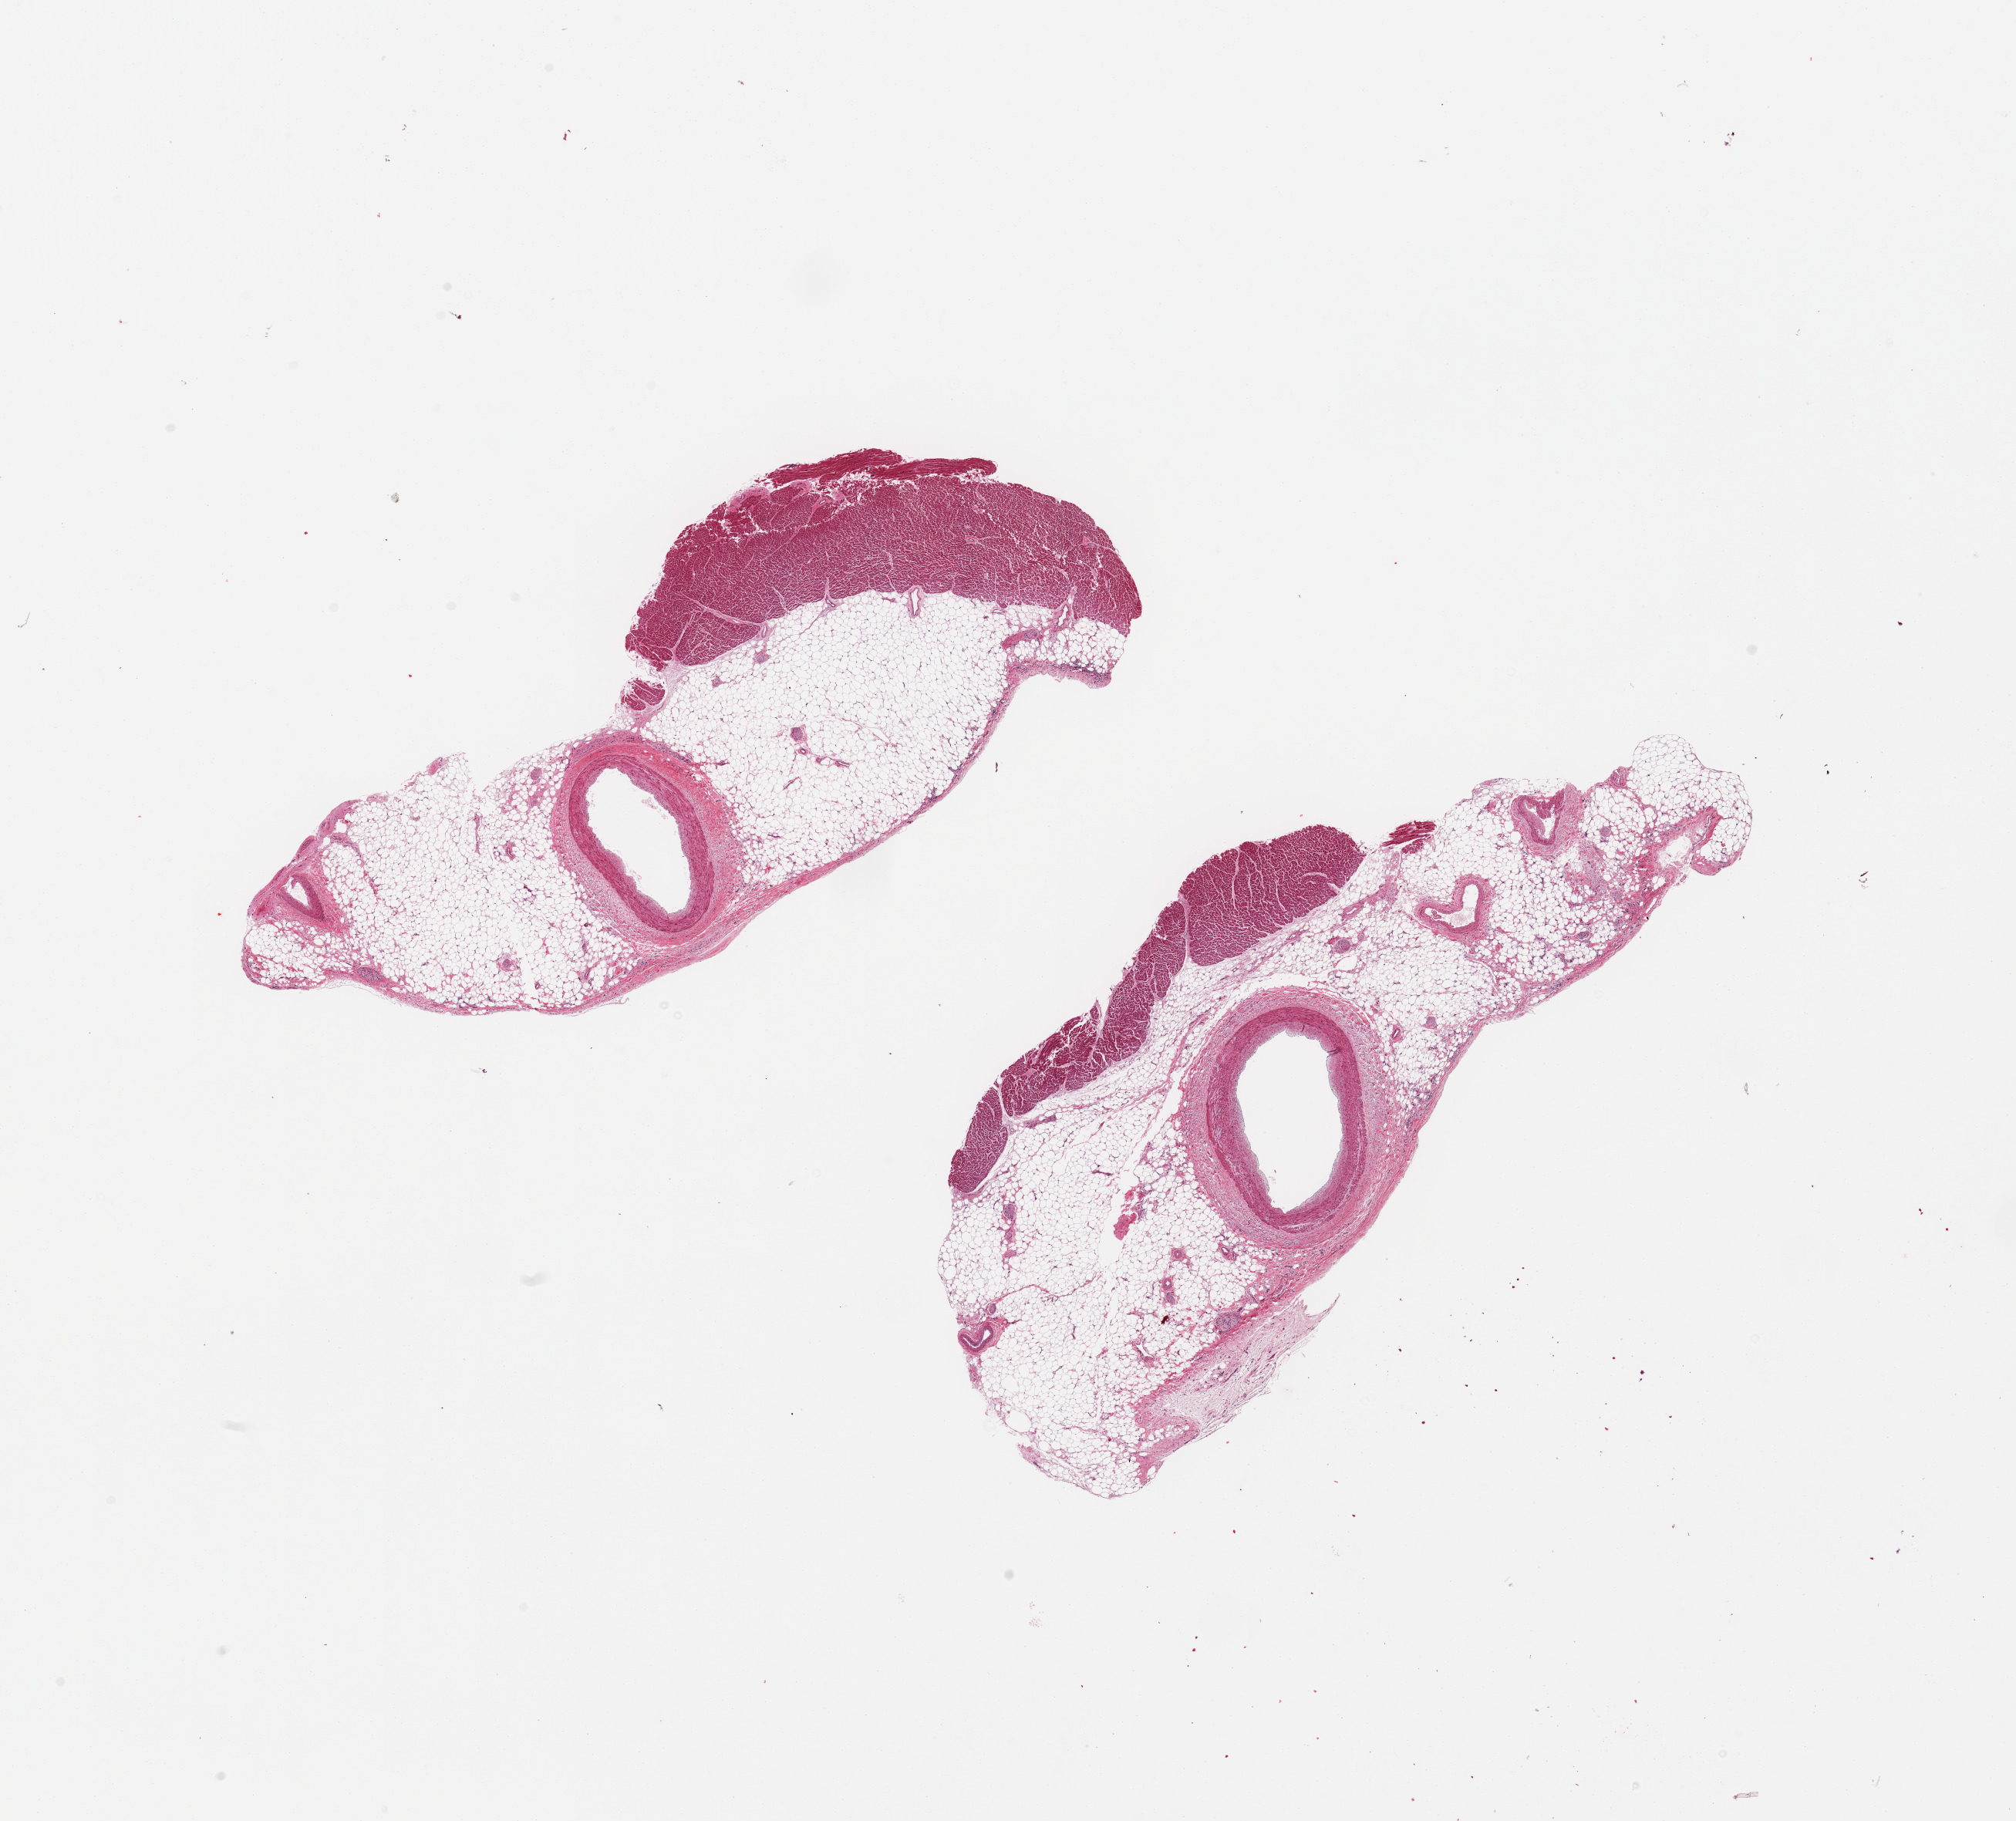
Digitized haematoxylin and eosin-stained section, whole scanned area (about 20.7 x 18.7 mm, from a 20x scan) shown as a low-resolution overview. Donor sex: female.
* specimen: PAXgene-fixed paraffin-embedded (PFPE) section; sampled site (target tissue): coronary artery; donor tissue sample